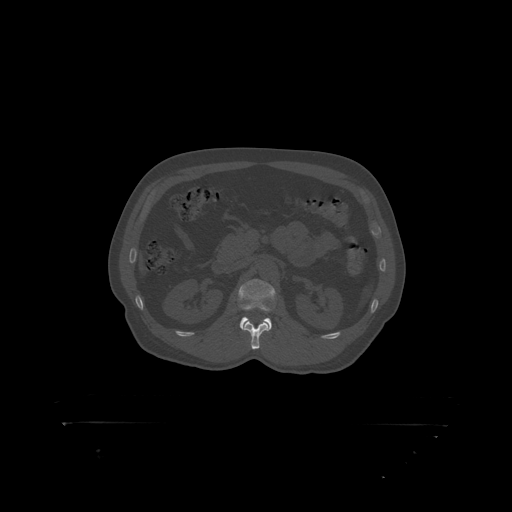
CT including the spine, one axial slice; position 311 of 399 along the scan axis; reconstruction kernel STANDARD; 120 kVp; bone window (W 1800 / L 400 HU); 1.25 mm slice thickness; 512 × 512 image matrix, field of view 650 × 650 mm. Male patient, age 46 years. From the clinical record (not read from this slice): primary cancer: skin.
Structures marked on this image (semi-automatically segmented with operator editing):
- L2 vertebra: bounding box <239,279,276,318> (left, top, right, bottom; pixels)